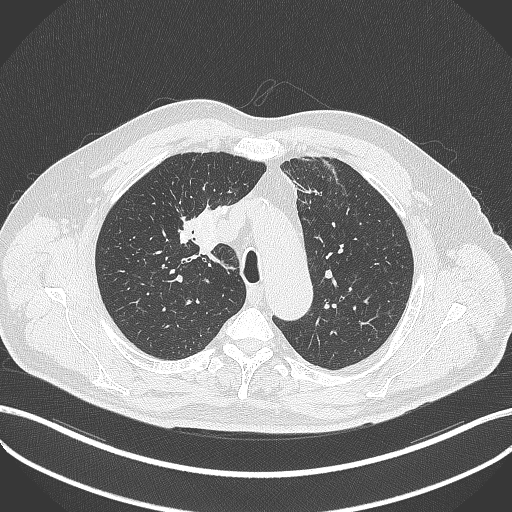
Chest CT, one axial slice. Slice 292 of 411 in the series (ordered by position). Lung window (W 1500 / L -600 HU). 1 mm slice thickness. 512 × 512 image matrix. Patient: male, 60 years. From the clinical record (not read from this slice): clinical TNM (as recorded): T1b N1 M0.
Outlined on this slice (bounding box drawn by a radiologist):
- lung tumour (recorded histology: squamous cell carcinoma): bounding box <191,196,224,261> (left, top, right, bottom; pixels)